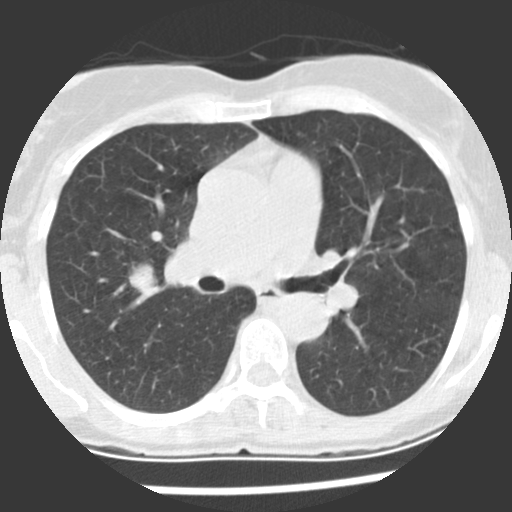
Low-dose screening chest CT, one axial slice; reconstruction kernel STANDARD; 120 kVp; lung window (W 1500 / L -600 HU); 512 × 512 image matrix, field of view 270 × 270 mm.
Annotated regions visible in this slice (expert manual segmentation):
- lesion 1 (tumor, upper lobe of right lung): bounding box [x1, y1, x2, y2] px = [129, 264, 157, 293]